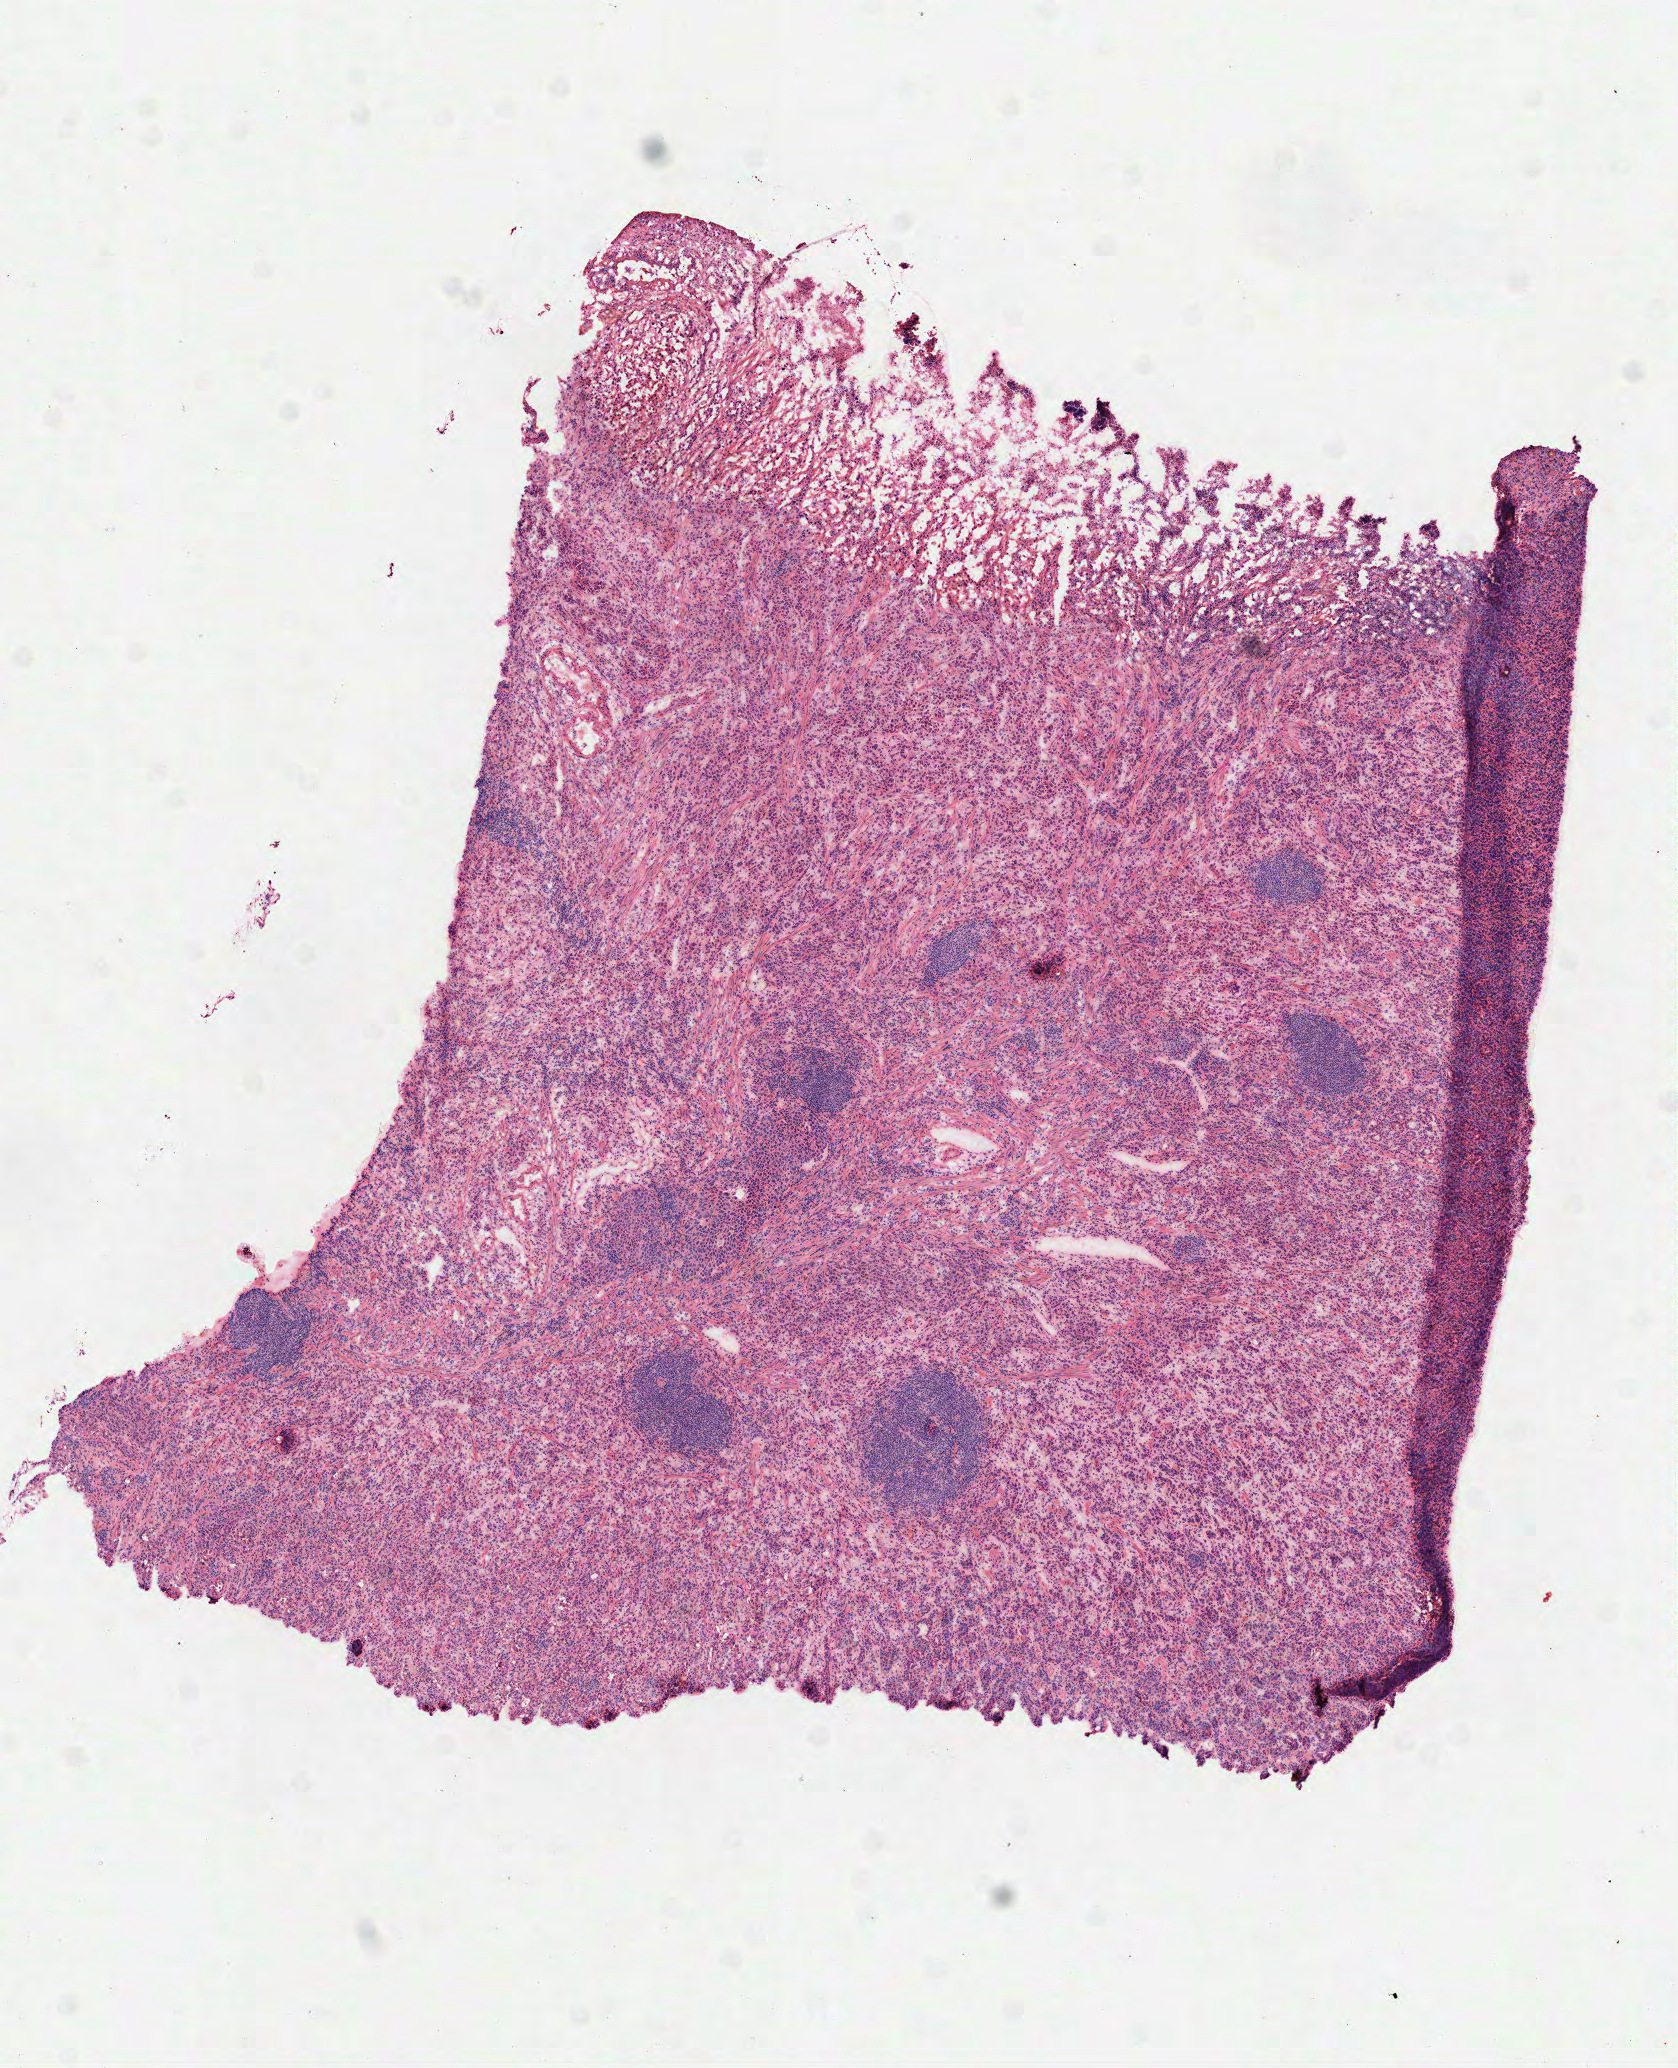
Whole-slide histology image, Hematoxylin and eosin (H&E) stained, whole scanned area (about 6.8 x 8.3 mm) shown as a low-resolution overview. Frozen section from the top of the tissue portion. Primary tumour sample from the stomach. Male, age 65 years at initial diagnosis. Histologic grade: G3 (poorly differentiated). Composition of this section per pathologist review: tumour cells 85%, tumour nuclei 70%, normal cells 0%, stromal cells 15%, necrosis 0%.
- lymph nodes positive (case pathology): 15 of 17 examined
- pathologic diagnosis: Carcinoma, diffuse type (body of stomach)